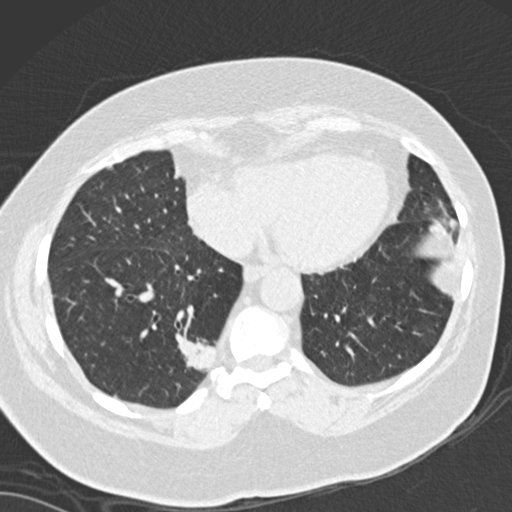
Chest CT (low-dose screening protocol), one axial image; baseline annual screen; lung window (W 1500 / L -600 HU); 2 mm slice thickness; 512 × 512 image matrix. Female, age 66 years at enrolment. Current smoker at enrolment.
Expert reader's lesion annotation, bounding box (x1, y1, x2, y2) in pixels: (143, 312, 237, 410). The screening reader recorded 3 non-calcified nodules or masses ≥4 mm on this exam (left lower lobe, left lower lobe, right lower lobe); which of them this box marks is not recorded. Official screen result: positive, change unspecified: nodule(s) >= 4 mm or enlarging nodule(s), mass(es), or other non-specific abnormalities suspicious for lung cancer.